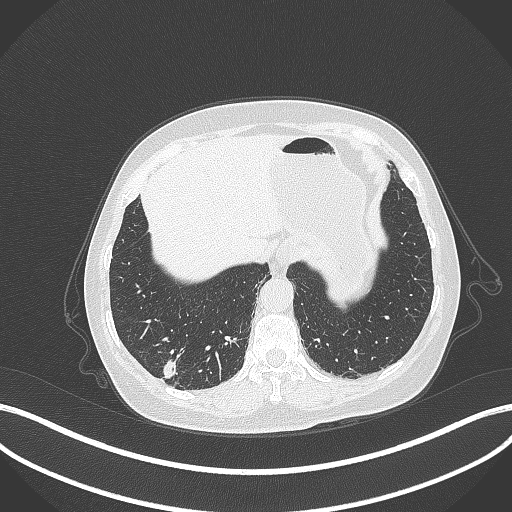
Chest CT, one axial slice; slice 50 of 333 in the series (ordered by position); reconstruction kernel B70f; lung window (W 1500 / L -600 HU); 1 mm slice thickness; 512 × 512 image matrix, field of view 400 × 400 mm. Patient: female, 69 years. From the clinical record (not read from this slice): clinical TNM (as recorded): T1b N0 M0; histopathological grade: G2-3.
Outlined on this slice (bounding box drawn by a radiologist):
- lung tumour (recorded histology: adenocarcinoma): bounding box (x1, y1, x2, y2) in pixels: (163, 357, 178, 380)